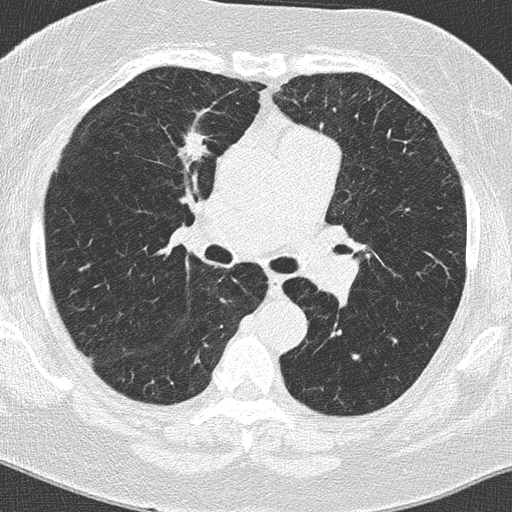
Axial slice from a low-dose chest CT screening exam. Second annual screen. Lung window (W 1500 / L -600 HU). 2 mm slice thickness. 120 kVp. 512 × 512 image matrix. Female, age 62 years at enrolment. Current smoker at enrolment.
Lesion marked by an expert reader, bounding box (x1, y1, x2, y2) in pixels: (160, 115, 227, 176). The screening reader recorded 2 non-calcified nodules or masses ≥4 mm on this exam (left lower lobe, right middle lobe); which of them this box marks is not recorded. Official screen result: positive, other. Lung cancer was diagnosed 396 days after this screen: adenocarcinoma, NOS, right upper lobe, moderately differentiated (G2), stage IA (AJCC 6th edition), 15 mm at pathology.